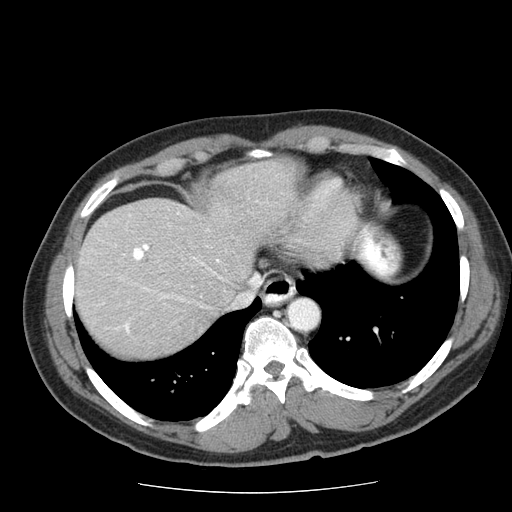
Contrast-enhanced abdominal CT (liver protocol), one axial slice. Position 57 of 85 along the scan axis. 120 kVp. Soft-tissue window (W 400 / L 40 HU). 2.5 mm slice thickness. 512 × 512 image matrix, field of view 360 × 360 mm. Case-level facts recorded for this patient, not image findings: diagnosis: hepatocellular carcinoma (patient treated with transarterial chemoembolisation; whether this scan precedes or follows treatment is not stated here); TNM stage (as recorded): Stage-IIIA; Child-Pugh class: A; tumour differentiation: well differentiated; tumour nodularity: multinodular.
Structures marked on this image (semi-automatic segmentation, software-assisted and operator-edited):
- liver parenchyma outside the tumour (the mass and vessels are separate outlines, so this box may not span the whole liver): box from (x=74, y=158) to (x=296, y=358) px
- liver vessels: (x=124, y=212)–(x=221, y=333)